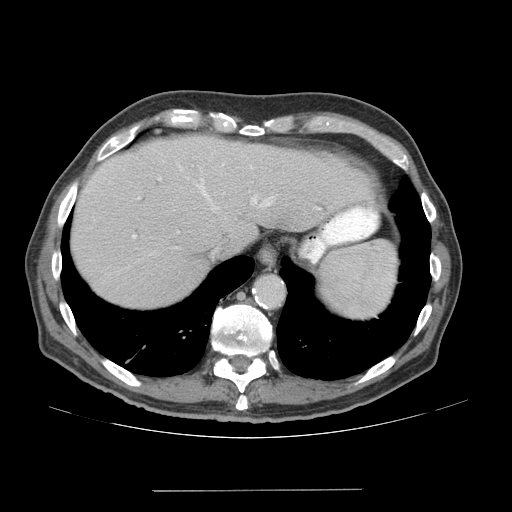
Contrast-enhanced abdominal CT (liver protocol), one axial slice; slice 57 of 77 in the series (ordered by position); reconstruction kernel STANDARD; soft-tissue window (W 400 / L 40 HU); 2.5 mm slice thickness; 512 × 512 image matrix. From the clinical record (not read from this slice): diagnosis: hepatocellular carcinoma (patient treated with transarterial chemoembolisation; whether this scan precedes or follows treatment is not stated here); TNM stage (as recorded): Stage-IVA; Child-Pugh class: A; tumour differentiation: well differentiated; tumour nodularity: uninodular.
Annotated regions visible in this slice (semi-automatically segmented with operator editing):
- abdominal aorta: box from (x=256, y=277) to (x=283, y=307) px
- liver parenchyma outside the tumour (the mass and vessels are separate outlines, so this box may not span the whole liver): (x=70, y=136)–(x=372, y=308)
- liver vessels: (x=132, y=164)–(x=320, y=238)